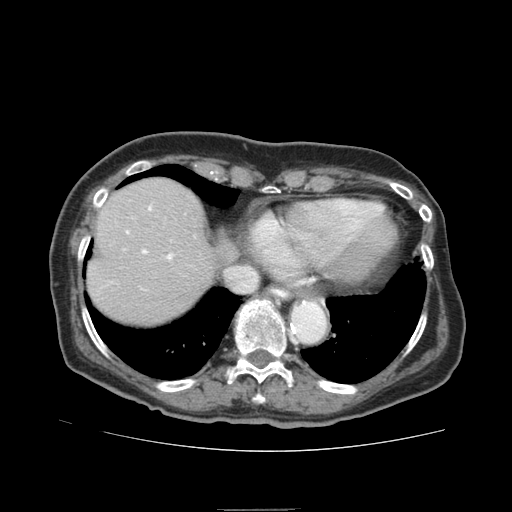
Contrast-enhanced abdominal CT (liver protocol), one axial slice. Slice 71 of 95 in the series (ordered by position). Reconstruction kernel STANDARD. 140 kVp. Soft-tissue window (W 400 / L 40 HU). 512 × 512 image matrix, field of view 360 × 360 mm. Case-level facts recorded for this patient, not image findings: diagnosis: hepatocellular carcinoma (patient treated with transarterial chemoembolisation; whether this scan precedes or follows treatment is not stated here); TNM stage (as recorded): Stage-IVA; Child-Pugh class: B; tumour differentiation: moderately differentiated; tumour nodularity: uninodular.
Outlined on this slice (semi-automatic segmentation, software-assisted and operator-edited):
- liver parenchyma outside the tumour (the mass and vessels are separate outlines, so this box may not span the whole liver): bounding box (x1, y1, x2, y2) in pixels: (86, 178, 216, 322)
- liver vessels: (126, 205, 174, 260)